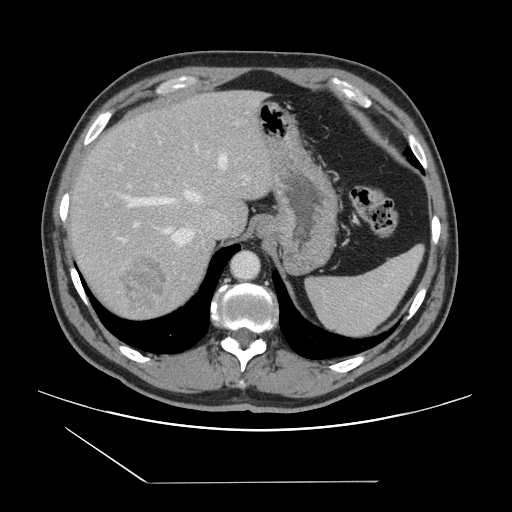
Contrast-enhanced abdominal CT, one axial slice. Slice 114 of 157 in the series (ordered by position). 120 kVp. Intravenous contrast given. Soft-tissue window (W 400 / L 40 HU). 512 × 512 image matrix. Male patient, age 61 years. Case-level facts recorded for this patient, not image findings: diagnosis: colorectal cancer liver metastases, imaged before liver resection; multiple liver metastases: yes; largest metastasis: 5.5 cm.
Structures marked on this image (manually delineated by an expert):
- hepatic veins: bounding box (x1, y1, x2, y2) in pixels: (121, 145, 227, 249)
- liver: (69, 91, 273, 319)
- planned liver remnant (the part of the liver to remain after resection): (70, 91, 236, 231)
- portal vein (with intrahepatic branches): (119, 143, 247, 241)
- liver metastasis: (117, 253, 170, 315)